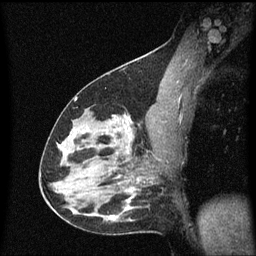
Breast MRI (dynamic contrast-enhanced), one sagittal slice. Slice 33 of 60 in the series (ordered by position). Dynamic contrast-enhanced series, image 2 of 3 at this slice position (ordered by acquisition). 1.5 T. TE 4.2 ms, TR 8.4 ms. 256 × 256 image matrix, field of view 200 × 200 mm. Patient: female, 38 years. From the clinical record (not read from this slice): setting: breast cancer imaged before/during neoadjuvant chemotherapy; receptor status: HR-positive, HER2-negative.
Structures marked on this image (semi-automatically segmented with operator editing):
- analysis volume of interest (the breast-tissue region the enhancement analysis was run in; not a lesion): box from (x=122, y=126) to (x=154, y=163) px
- tumour enhancement mask (voxels above the 70 % enhancement threshold inside the analysis volume of interest): (x=125, y=126)–(x=131, y=155)